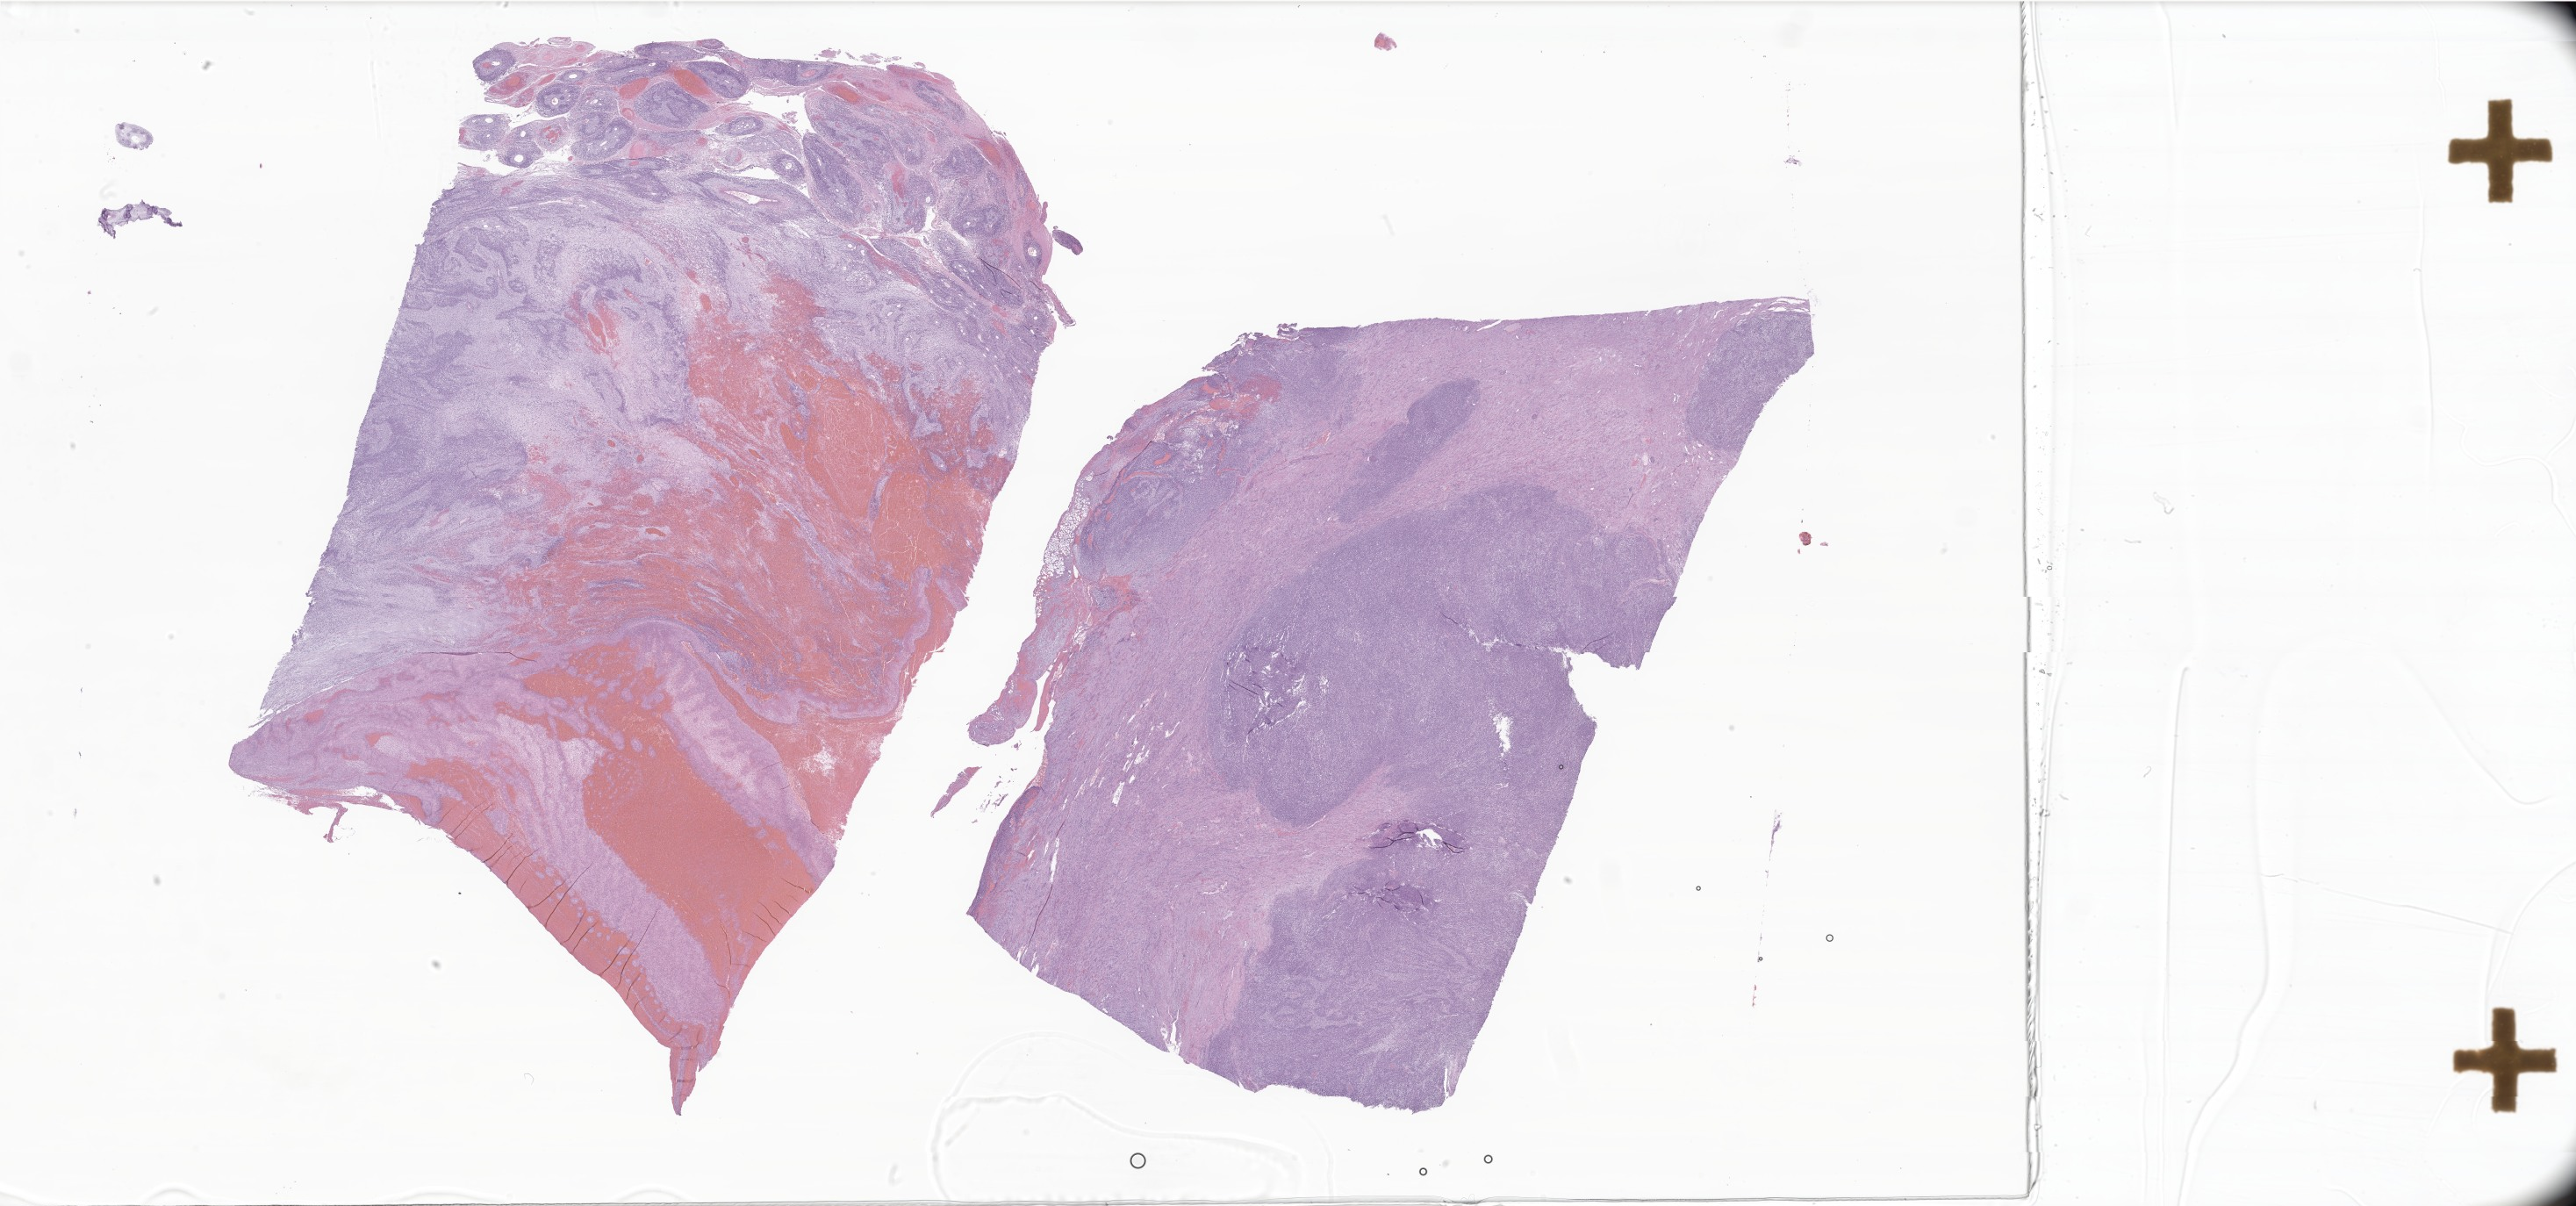
Digitized H&E-stained section of tumor tissue from the kidney — whole scanned area (about 49.5 x 23.2 mm) shown as a low-resolution overview; FFPE section. Patient: male, age 763 days.
* diagnosis (ICD-O-3 morphology term): Rhabdomyosarcoma, NOS